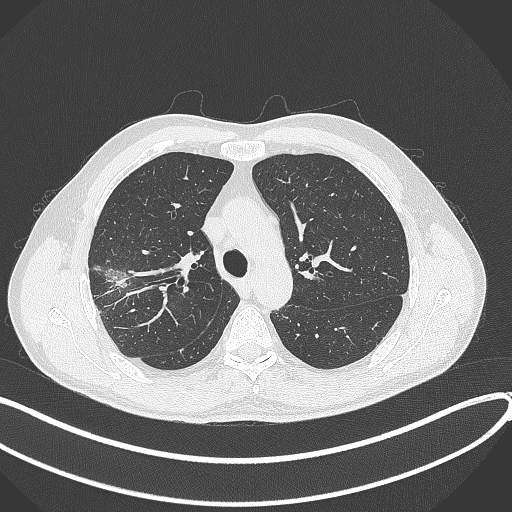
Chest CT, one axial slice; position 298 of 381 along the scan axis; 120 kVp; lung window (W 1500 / L -600 HU); 1 mm slice thickness; 512 × 512 image matrix. Male patient, age 62 years. From the clinical record (not read from this slice): clinical TNM (as recorded): T1c N0 M0; histopathological grade: G2-3.
Structures marked on this image (bounding box drawn by a radiologist):
- lung tumour (recorded histology: adenocarcinoma): box from (x=101, y=262) to (x=131, y=294) px